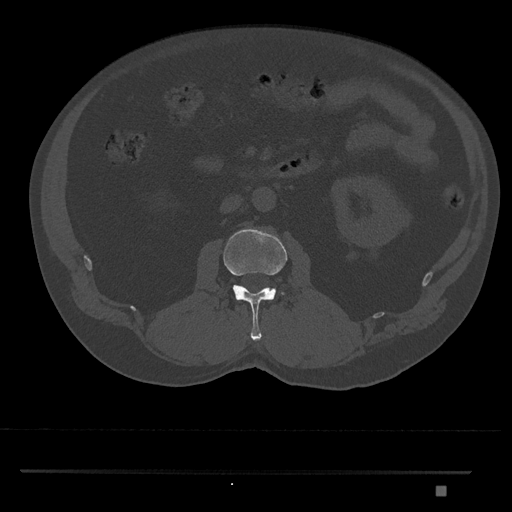
CT including the spine, one axial slice; position 743 of 1134 along the scan axis; 120 kVp; bone window (W 1800 / L 400 HU); 512 × 512 image matrix, field of view 429 × 429 mm. Patient: male, 65 years. From the clinical record (not read from this slice): primary cancer: prostate.
Structures marked on this image (semi-automatic segmentation, software-assisted and operator-edited):
- L2 vertebra: bounding box (x1, y1, x2, y2) in pixels: (223, 228, 287, 341)